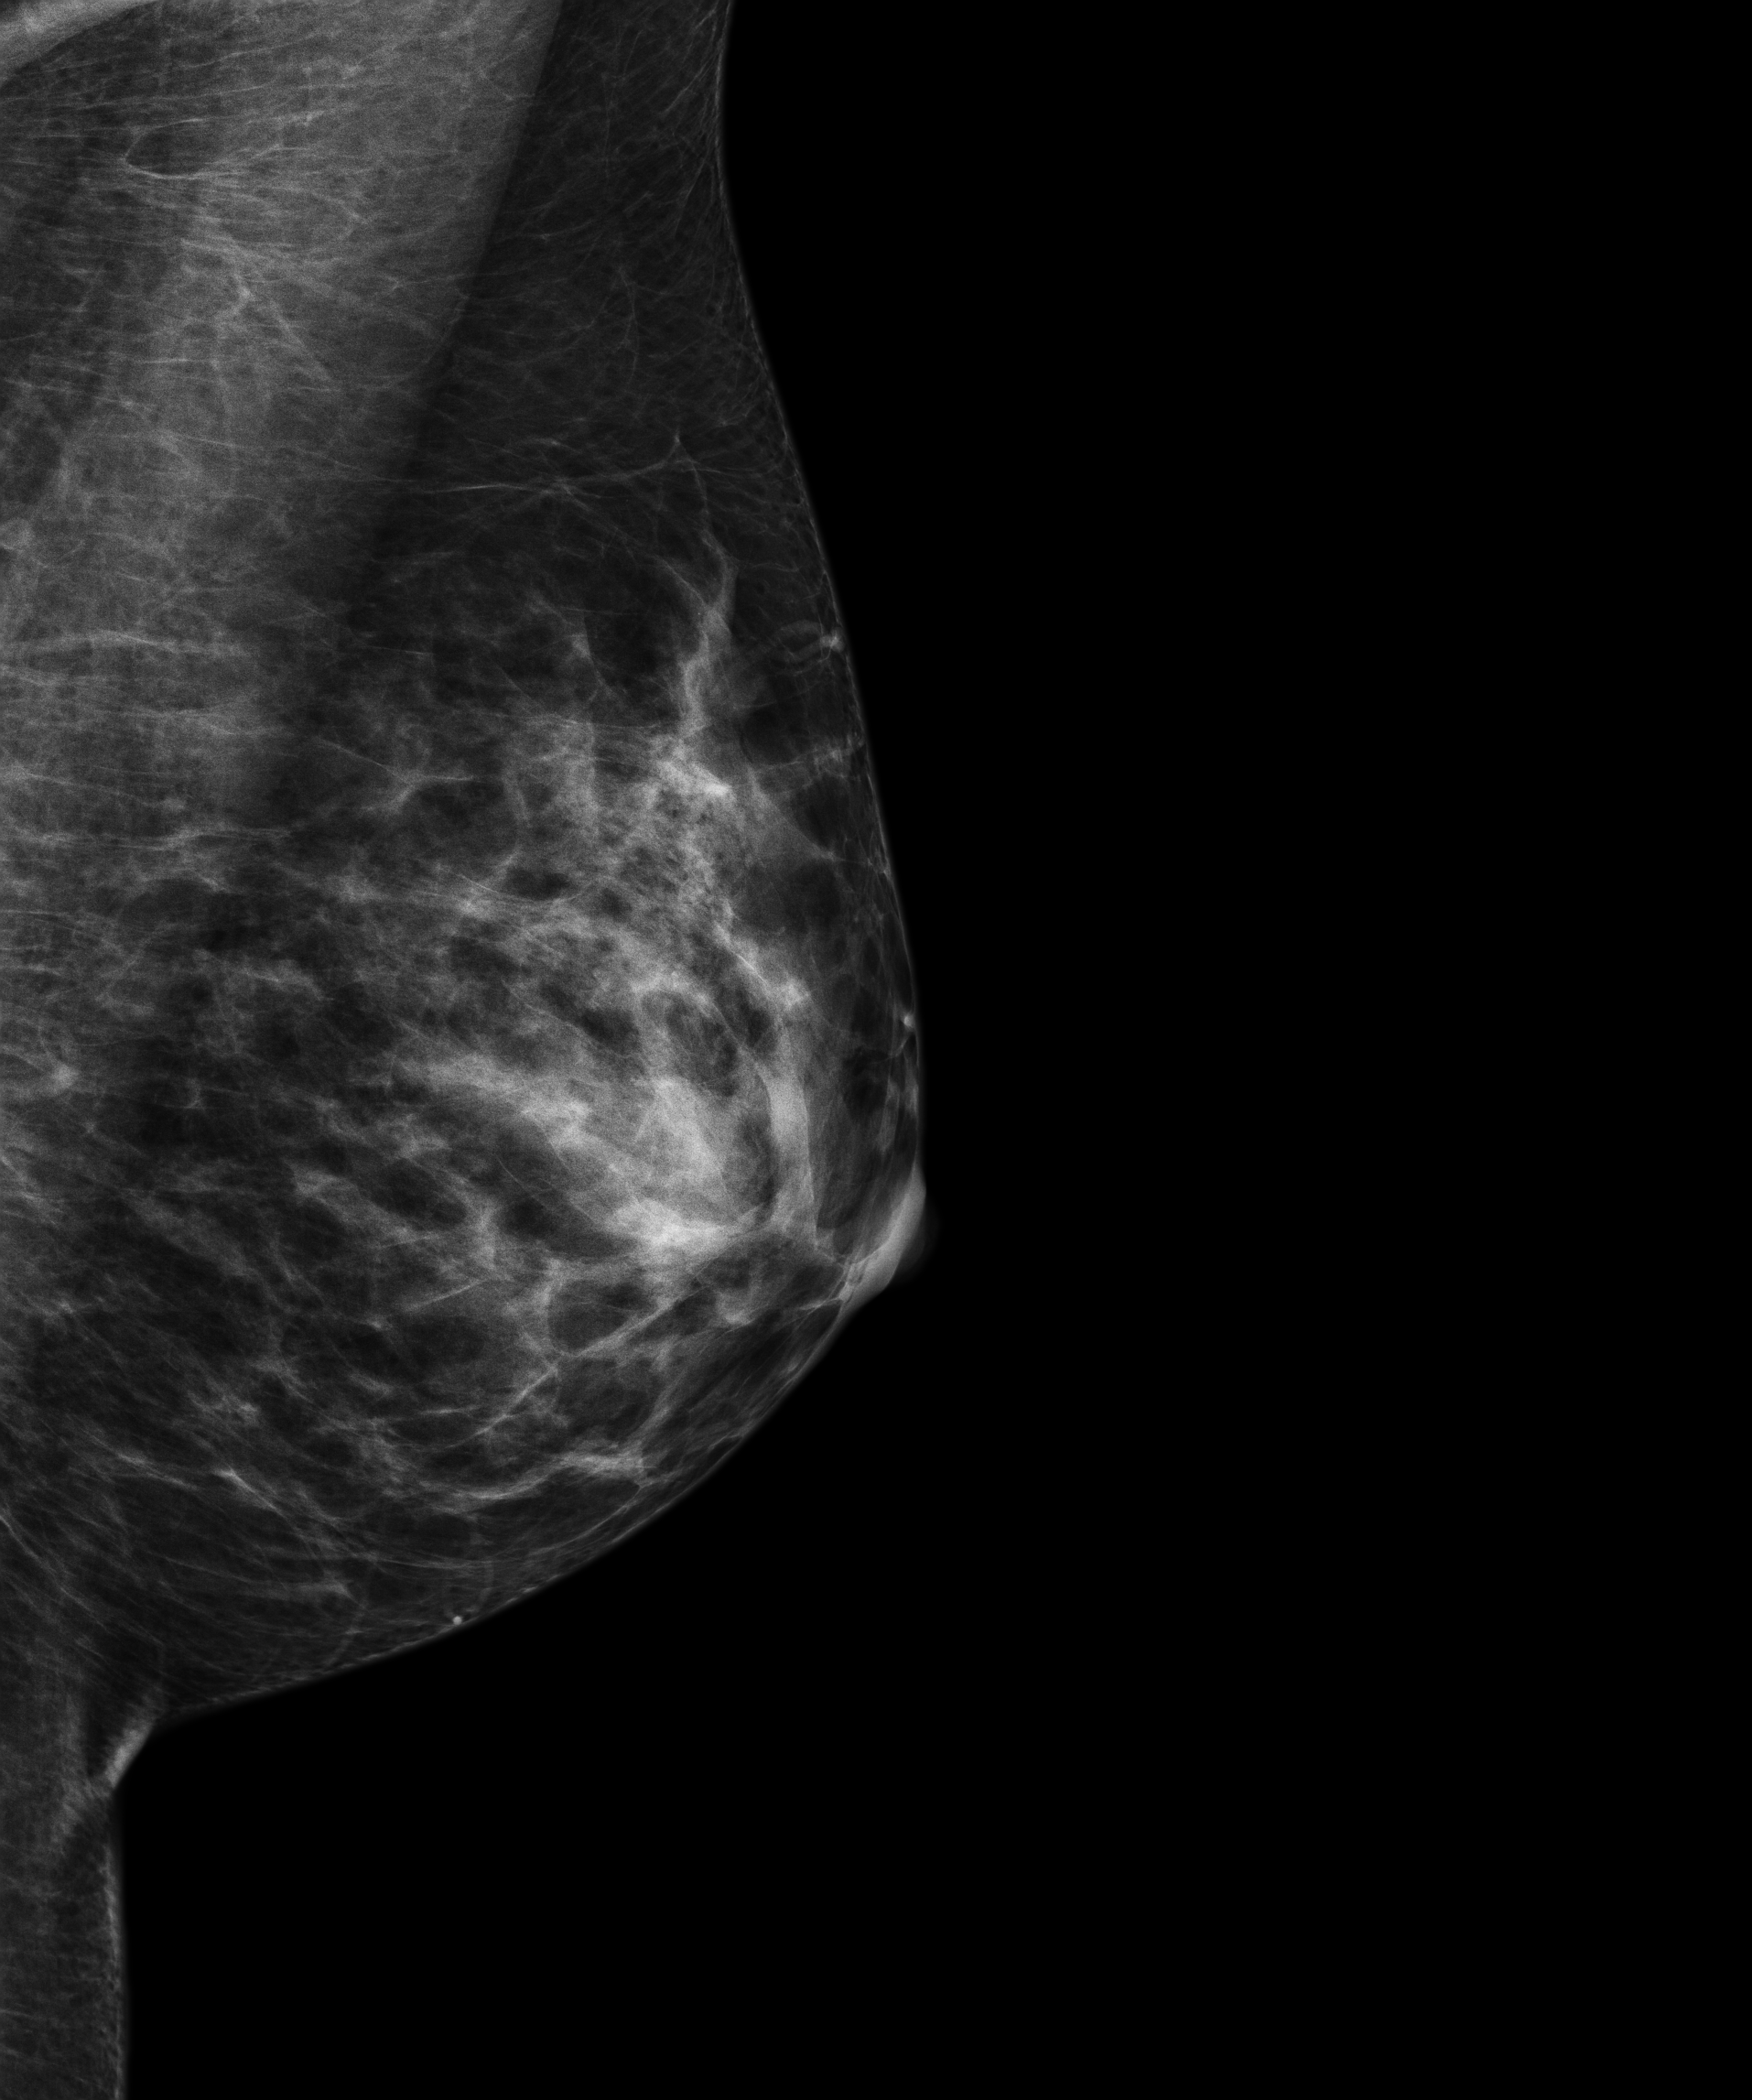
Full-field digital mammogram (FFDM), left breast, mediolateral oblique (MLO) view, screening examination, compressed breast thickness 50 mm, system: Senographe Essential ADS_56.21.3. Patient aged 42 years (female).
BI-RADS breast density category at the screening exam (both breasts, scale 1–4): 3. Final BI-RADS category for the screening round (tomosynthesis exam, both breasts): category 1. Recall: no recall after this screen.